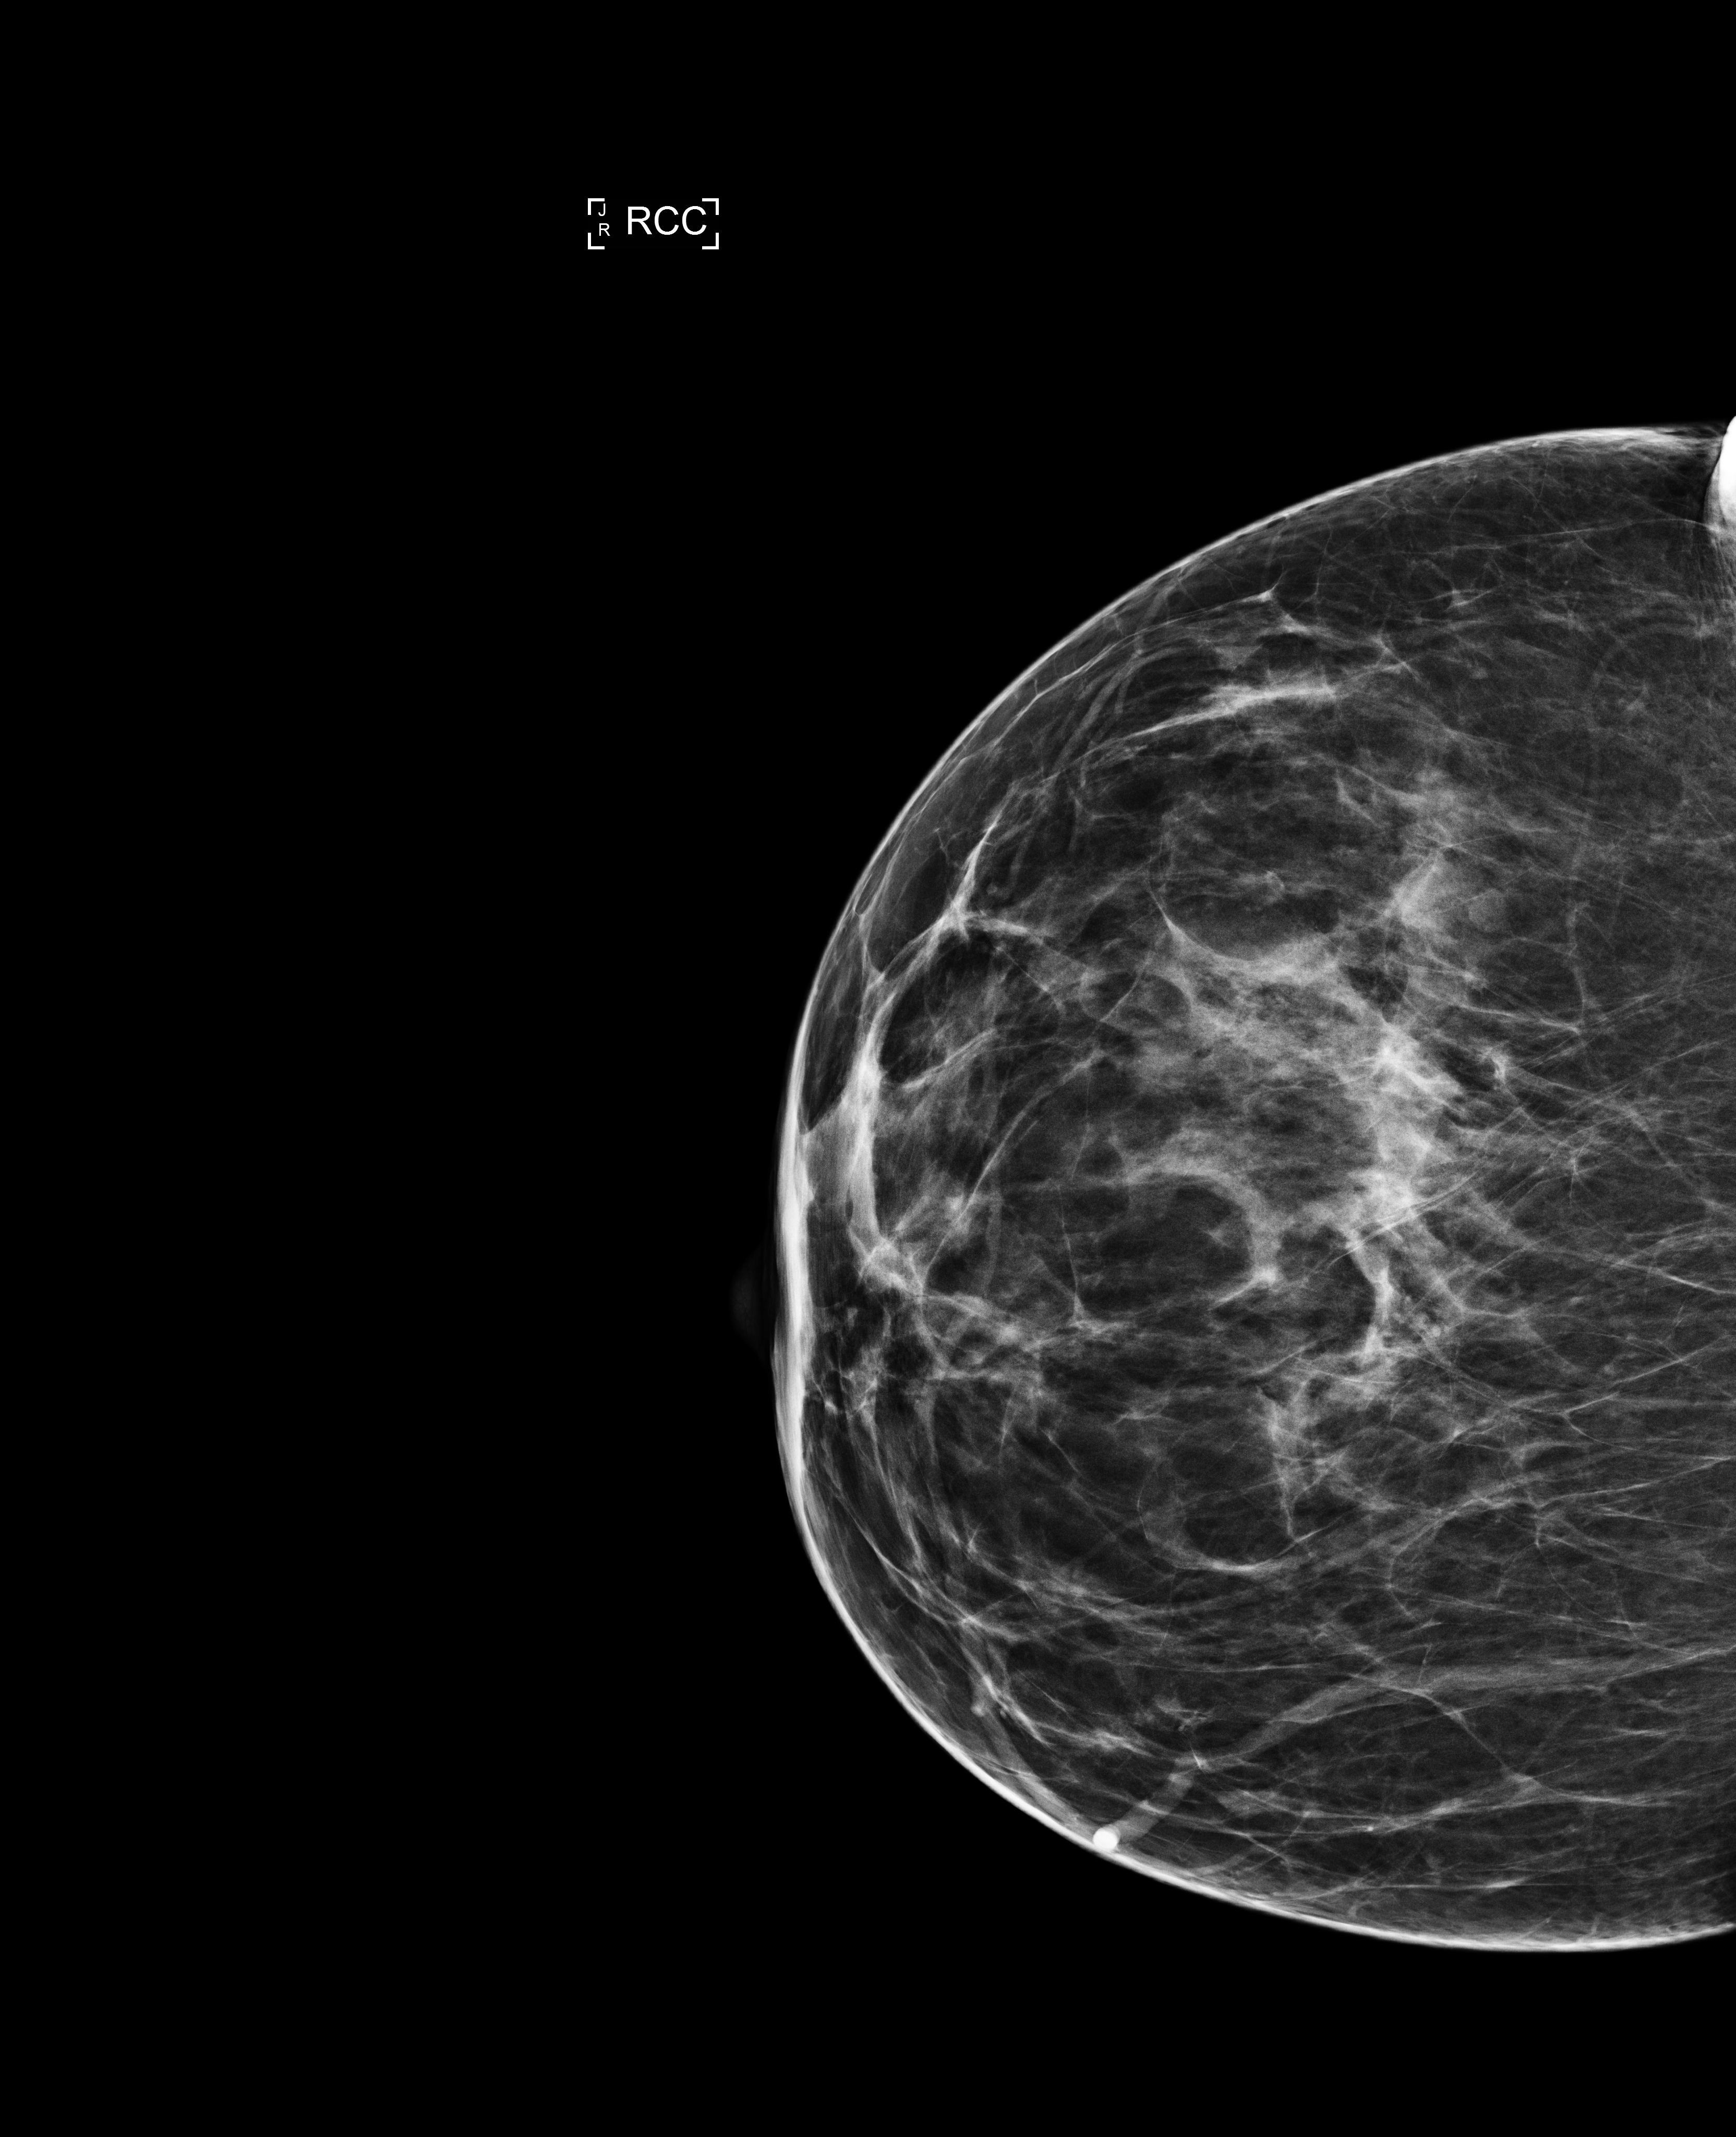
Digital mammogram (FFDM); right breast; CC view; screening examination; compressed breast thickness 62 mm. Female patient, age 50 years.
Breast density at the screening exam (both breasts): heterogeneously dense (BI-RADS density category c). Final BI-RADS assessment for this screening round (tomosynthesis exam, both breasts): category 1. Recall: no recall after this screen.